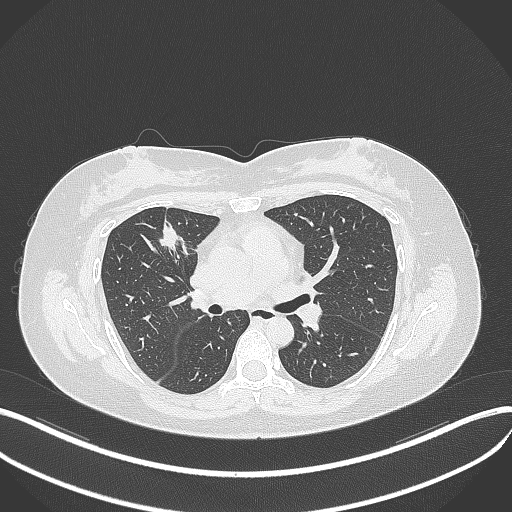
Chest CT, one axial slice. Slice 185 of 273 in the series (ordered by position). Reconstruction kernel B70f. 120 kVp. Lung window (W 1500 / L -600 HU). 1 mm slice thickness. 512 × 512 image matrix. Patient: female, 42 years. From the clinical record (not read from this slice): clinical TNM (as recorded): T1b N0 M0.
Outlined on this slice (bounding box drawn by a radiologist):
- lung tumour (recorded histology: adenocarcinoma): bounding box <155,218,188,260> (left, top, right, bottom; pixels)